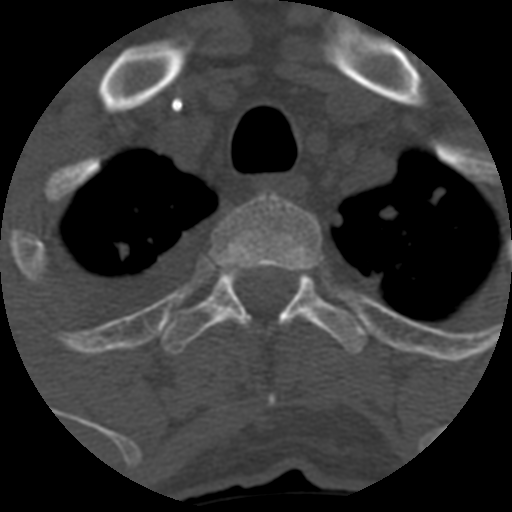
CT including the spine, one axial slice; slice 495 of 708 in the series (ordered by position); reconstruction kernel STANDARD; one of 3 acquisitions stored at this slice position; bone window (W 1800 / L 400 HU); 1.25 mm slice thickness; 512 × 512 image matrix, field of view 160 × 160 mm. Patient age 55 years. Case-level facts recorded for this patient, not image findings: primary cancer: colon.
Annotated regions visible in this slice (semi-automatically segmented with operator editing):
- T2 vertebra: bounding box (x1, y1, x2, y2) in pixels: (211, 195, 323, 273)
- T3 vertebra: (161, 267, 367, 355)